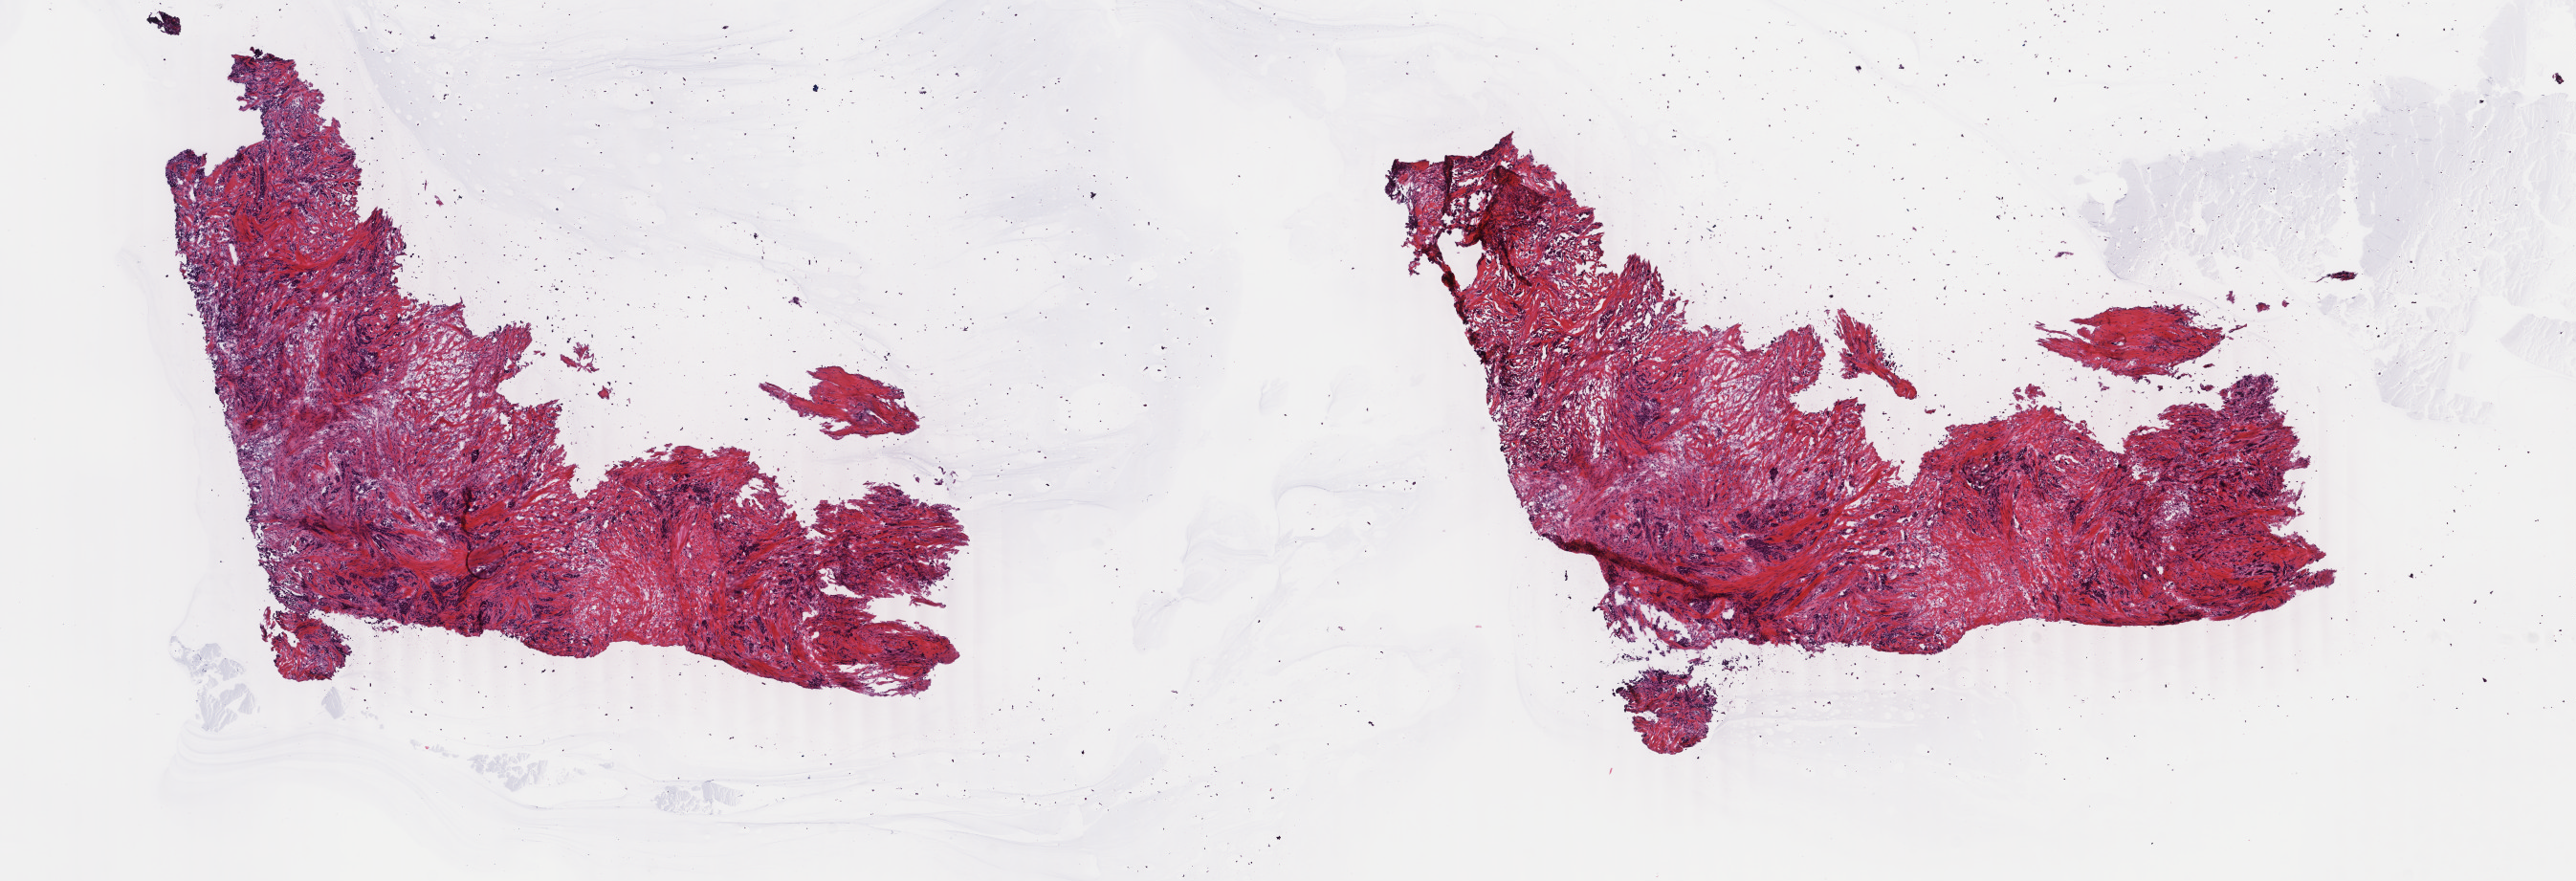
Whole-slide histology image, Hematoxylin and eosin (H&E) stained, a low-resolution overview of the entire scanned area, about 21.4 x 7.3 mm (from a 40x scan). Frozen section. Breast, primary tumour sample. Patient: female, age at initial diagnosis 59 years. Pathologist review of this section (percent, as recorded): tumour cells 70%, tumour nuclei 70%, normal cells 0%, stromal cells 30%, necrosis 0%. Inflammatory infiltration, as recorded: lymphocyte infiltration 2%, monocyte infiltration 1%, neutrophil infiltration 1%.
Lymph nodes positive (case pathology): 2 of 19 examined. Diagnosis: Infiltrating duct carcinoma, NOS. AJCC pathologic stage: IIB. TNM: T2 N1a M0.